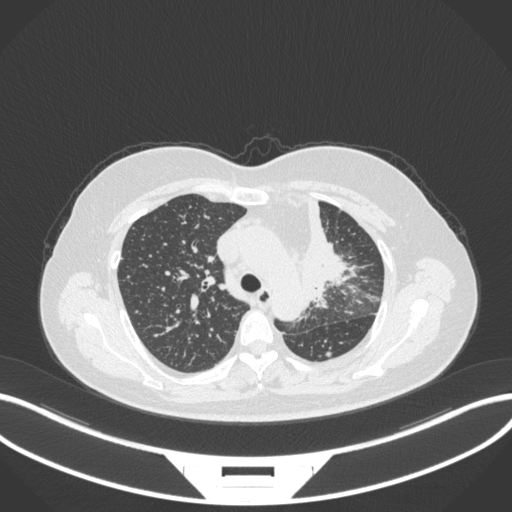
Chest CT, one axial slice; position 239 of 348 along the scan axis; reconstruction kernel B31f; 120 kVp; lung window (W 1500 / L -600 HU); 1 mm slice thickness; 512 × 512 image matrix, field of view 400 × 400 mm. Female patient, age 49 years. Case-level facts recorded for this patient, not image findings: clinical TNM (as recorded): T1c N0 M1.
Annotated regions visible in this slice (bounding box drawn by a radiologist):
- lung tumour (recorded histology: adenocarcinoma): box from (x=294, y=196) to (x=363, y=313) px